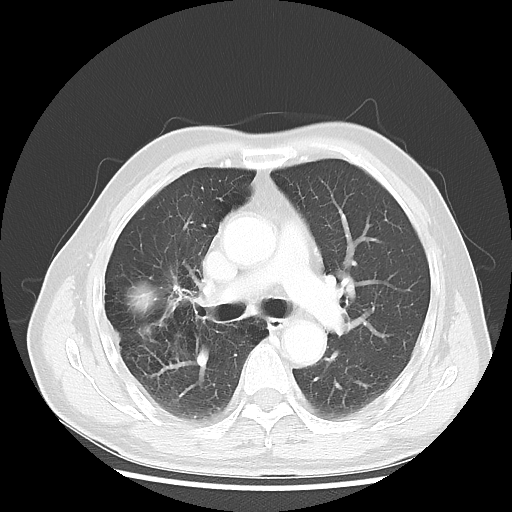
Chest CT, one axial slice; slice 30 of 50 in the series (ordered by position); reconstruction kernel LUNG; lung window (W 1500 / L -600 HU); 512 × 512 image matrix, field of view 360 × 360 mm. Patient: male, 69 years. From the clinical record (not read from this slice): clinical TNM (as recorded): T3 N0 M0; histopathological grade: G3.
Outlined on this slice (bounding box drawn by a radiologist):
- lung tumour (recorded histology: adenocarcinoma): bounding box (x1, y1, x2, y2) in pixels: (123, 275, 162, 318)